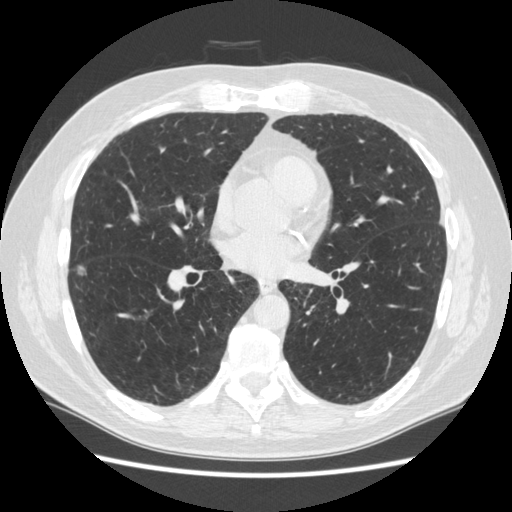
Low-dose screening chest CT, one axial slice. Position 124 of 267 along the scan axis. Reconstruction kernel STANDARD. Lung window (W 1500 / L -600 HU). 512 × 512 image matrix, field of view 360 × 360 mm.
Structures marked on this image (manually delineated by an expert):
- lesion 2 (nodule, lower lobe of right lung): bounding box [x1, y1, x2, y2] px = [78, 267, 87, 277]